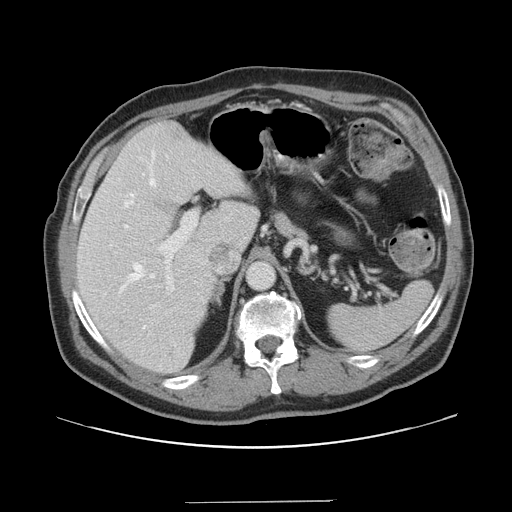
Contrast-enhanced abdominal CT, one axial slice. Slice 101 of 151 in the series (ordered by position). Soft-tissue window (W 400 / L 40 HU). 2.5 mm slice thickness. 512 × 512 image matrix, field of view 399 × 399 mm. Male patient, age 63 years. Case-level facts recorded for this patient, not image findings: diagnosis: colorectal cancer liver metastases, imaged before liver resection; multiple liver metastases: no.
Outlined on this slice (outlined manually by an expert reader):
- hepatic veins: bounding box (x1, y1, x2, y2) in pixels: (120, 150, 176, 345)
- liver: (78, 122, 259, 373)
- planned liver remnant (the part of the liver to remain after resection): (78, 122, 258, 373)
- portal vein (with intrahepatic branches): (150, 211, 197, 308)